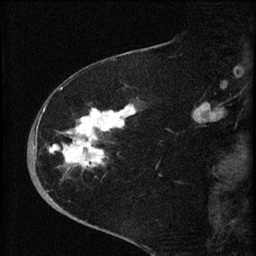
Breast MRI (dynamic contrast-enhanced), one sagittal slice; slice 22 of 60 in the series (ordered by position); dynamic contrast-enhanced series, image 2 of 4 at this slice position (ordered by acquisition); 1.5 T; TE 4.2 ms, TR 8.2 ms; 2 mm slice thickness; 256 × 256 image matrix, field of view 180 × 180 mm. Female patient, age 71 years.
Annotated regions visible in this slice (semi-automatically segmented with operator editing):
- analysis volume of interest (the breast-tissue region the enhancement analysis was run in; not a lesion): bounding box <35,75,144,190> (left, top, right, bottom; pixels)
- tumour enhancement mask (voxels above the 70 % enhancement threshold inside the analysis volume of interest): <44,90,136,169>